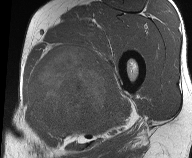
MRI of an extremity soft-tissue mass, one axial slice; slice 33 of 61 in the series (ordered by position); MR volume resampled by the dataset authors to the PET/CT grid (not the native acquisition matrix); 192 × 158 image matrix, field of view 187 × 154 mm. Male patient. Case-level facts recorded for this patient, not image findings: histological type: pleiomorphic liposarcoma; grade: high; site of the primary tumour: left thigh.
Structures marked on this image (expert contour drawn on MRI and transferred to this co-registered scan by the dataset authors):
- gross tumour volume including surrounding oedema: bounding box (x1, y1, x2, y2) in pixels: (27, 43, 119, 138)
- gross tumour volume (mass): (27, 44, 117, 129)